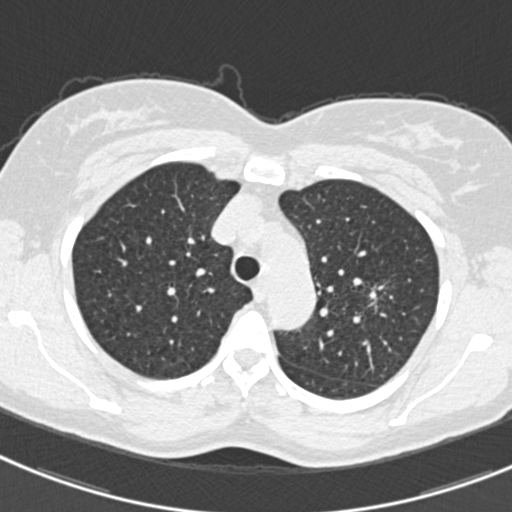
Low-dose screening chest CT, one axial slice; position 240 of 309 along the scan axis; reconstruction kernel B30f; 120 kVp; lung window (W 1500 / L -600 HU); 1 mm slice thickness; 512 × 512 image matrix.
Outlined on this slice (expert manual segmentation):
- lesion 1 (tumor, upper lobe of left lung): box from (x=371, y=293) to (x=375, y=299) px